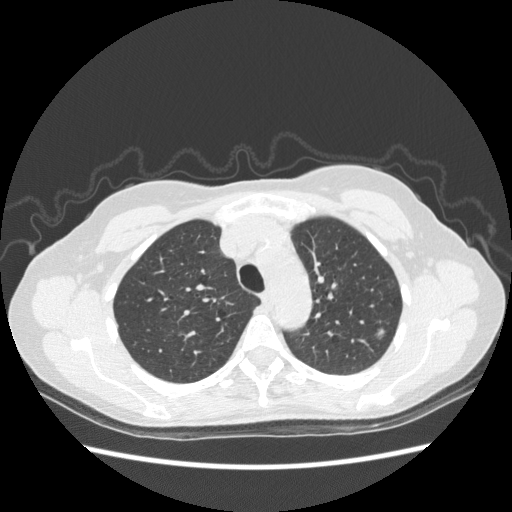
Axial slice from a low-dose chest CT screening exam, first (baseline) screen, lung window (W 1500 / L -600 HU), 1.25 mm slice thickness, standard (soft-tissue) reconstruction kernel (STANDARD), slice 72 of 270 in the series. Female, age 61 years at enrolment.
• Expert reader's lesion annotation, bounding box <357,321,394,352> (left, top, right, bottom; pixels).
• Reader record for this screening exam (exam-level; its link to the box is not recorded): non-calcified nodule or mass ≥4 mm, left upper lobe, 7 × 6 mm, poorly defined margins, ground glass attenuation.
• Official screen result: positive, change unspecified: nodule(s) >= 4 mm or enlarging nodule(s), mass(es), or other non-specific abnormalities suspicious for lung cancer.
• Lung cancer was diagnosed 484 days after this screen (after the second annual screen): bronchiolo-alveolar adenocarcinoma, NOS, left upper lobe, well differentiated (G1), stage IA (AJCC 6th edition), 8 mm at pathology.